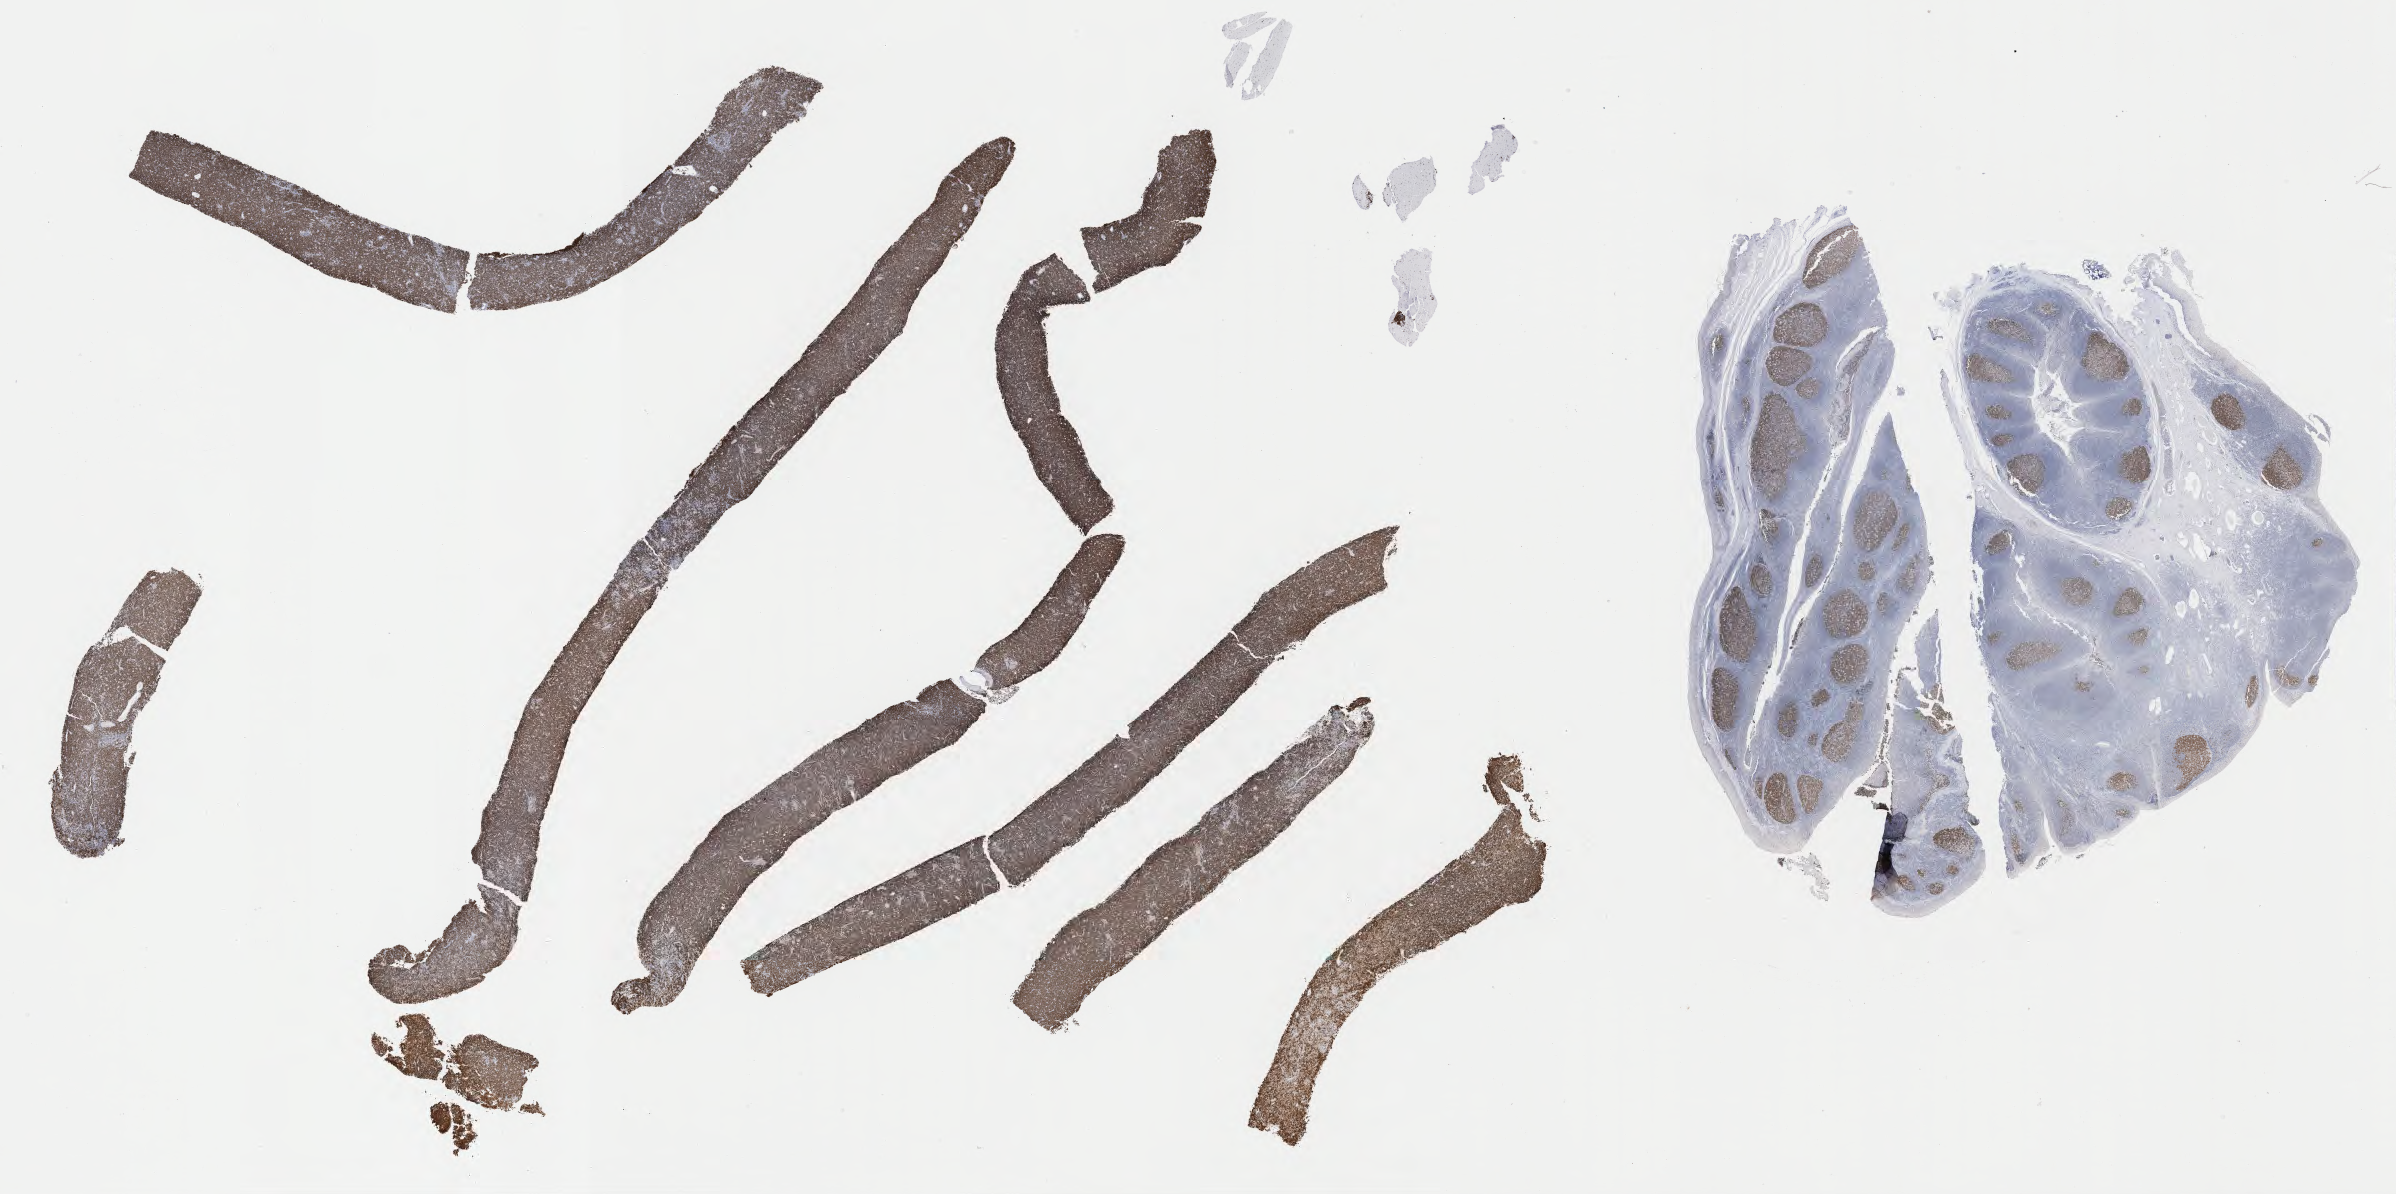
Immunohistochemistry (IHC) whole-slide image stained for BCL6 — shown as a low-resolution overview of the whole scanned area (about 38.8 x 19.3 mm). Tumor tissue. Male patient, aged 29.
• histologic diagnosis: Burkitt lymphoma, NOS